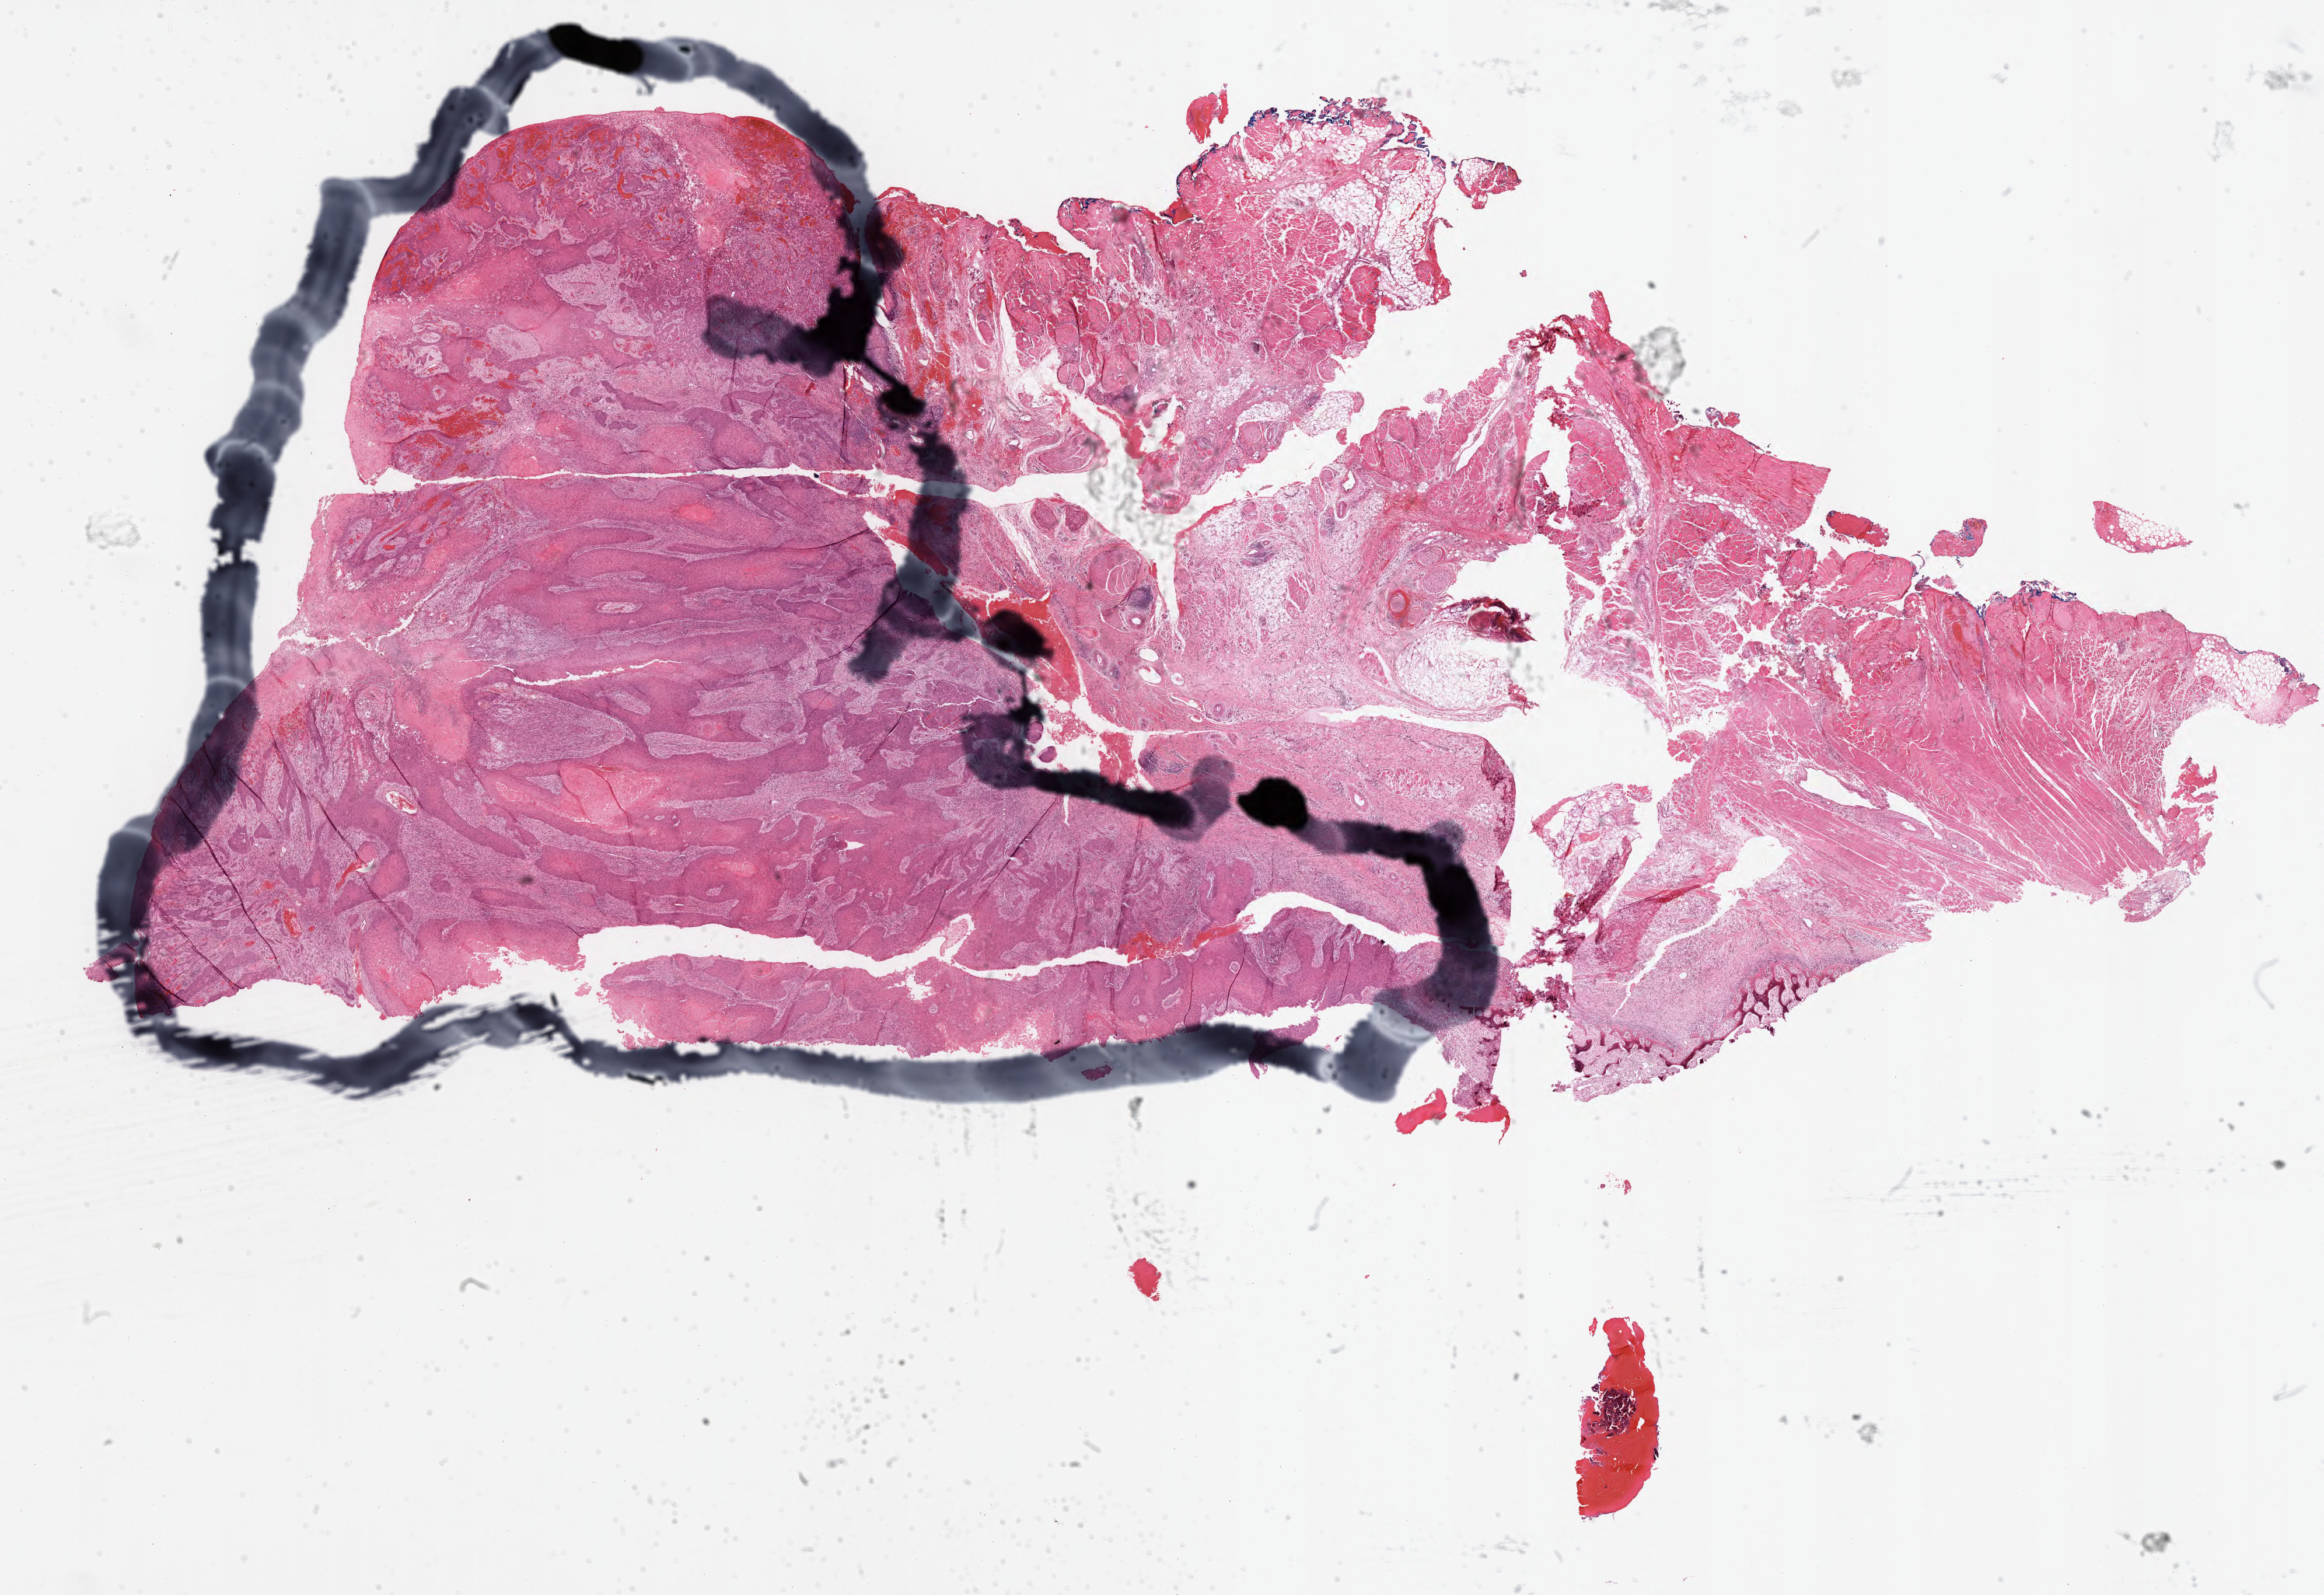
Whole-slide histology image, Hematoxylin and eosin (H&E) stained, whole scanned area (about 31.3 x 21.5 mm, acquisition: 40x scan) shown as a low-resolution overview, formalin-fixed paraffin-embedded (FFPE) diagnostic section, sample: primary tumour, head and neck. Patient: female, age at initial diagnosis 47 years.
Histologic diagnosis: Squamous cell carcinoma, NOS (floor of mouth, NOS).